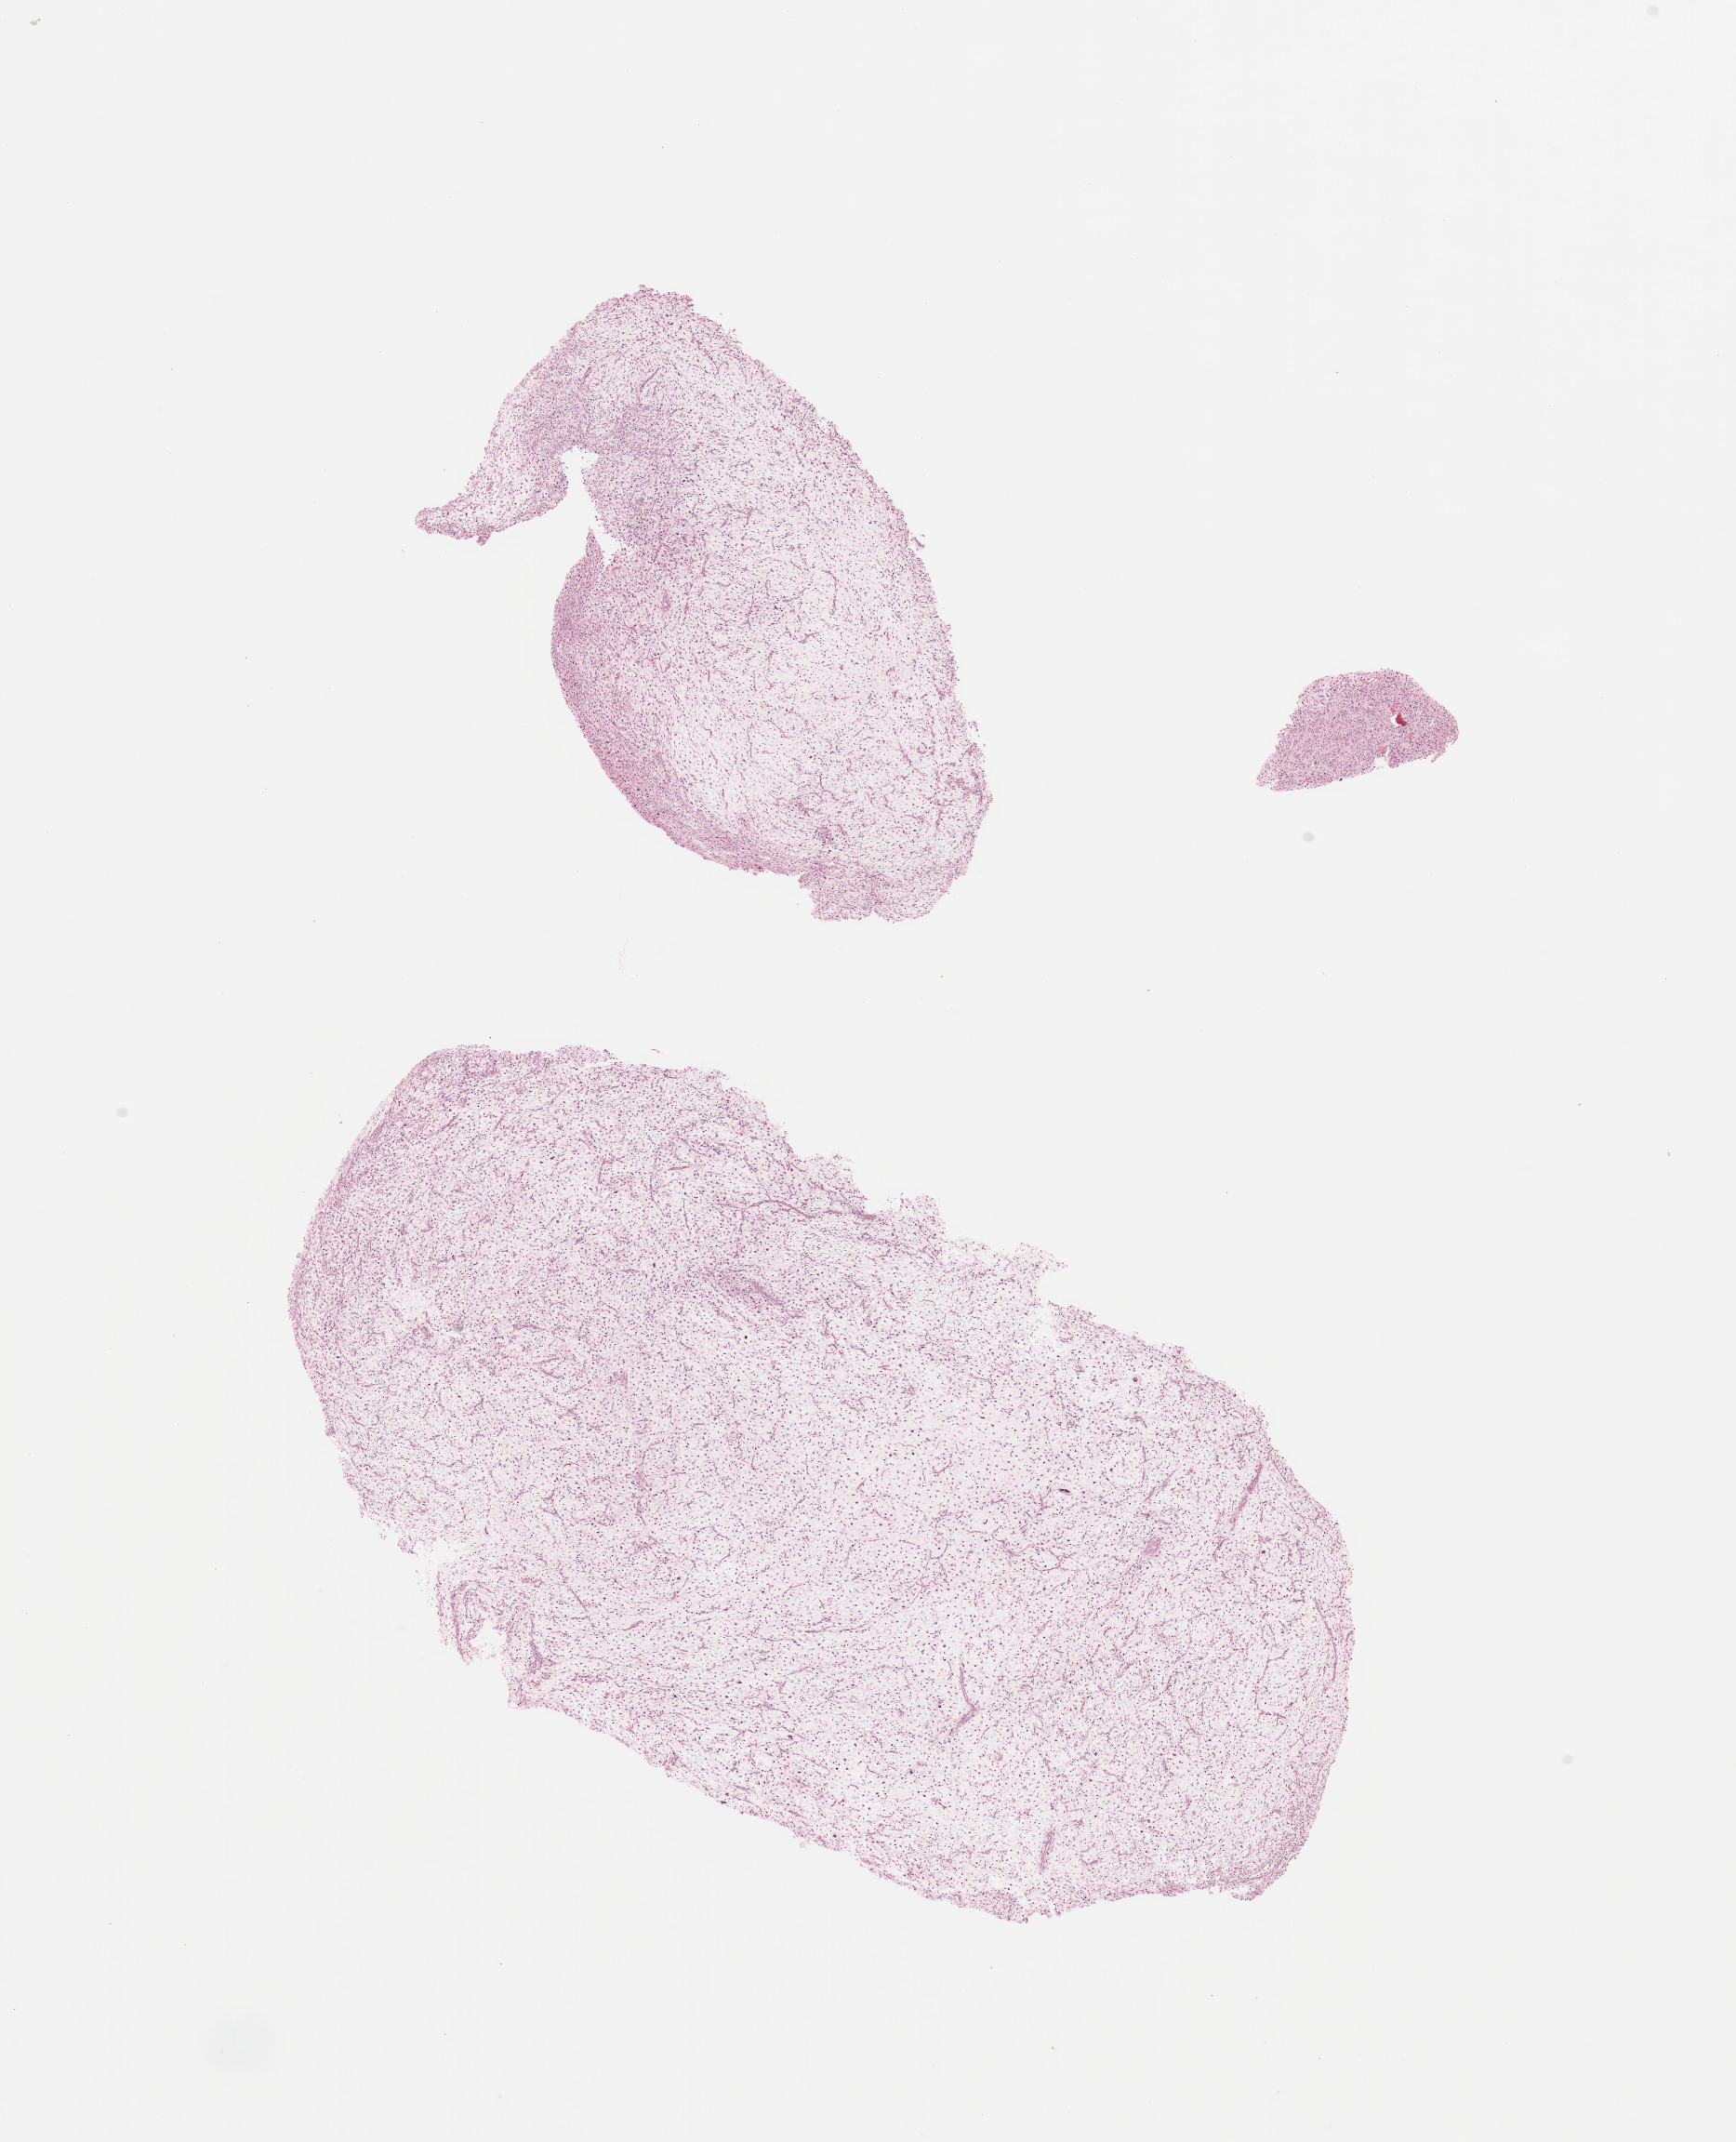
Digitized H&E-stained tissue section (whole slide) — shown as a low-resolution overview of the whole scanned area (about 14.8 x 18.2 mm); tumour tissue sample. 65-year-old male patient.
Patient diagnosis (cohort enrolment): sarcoma (site not recorded at cohort level).